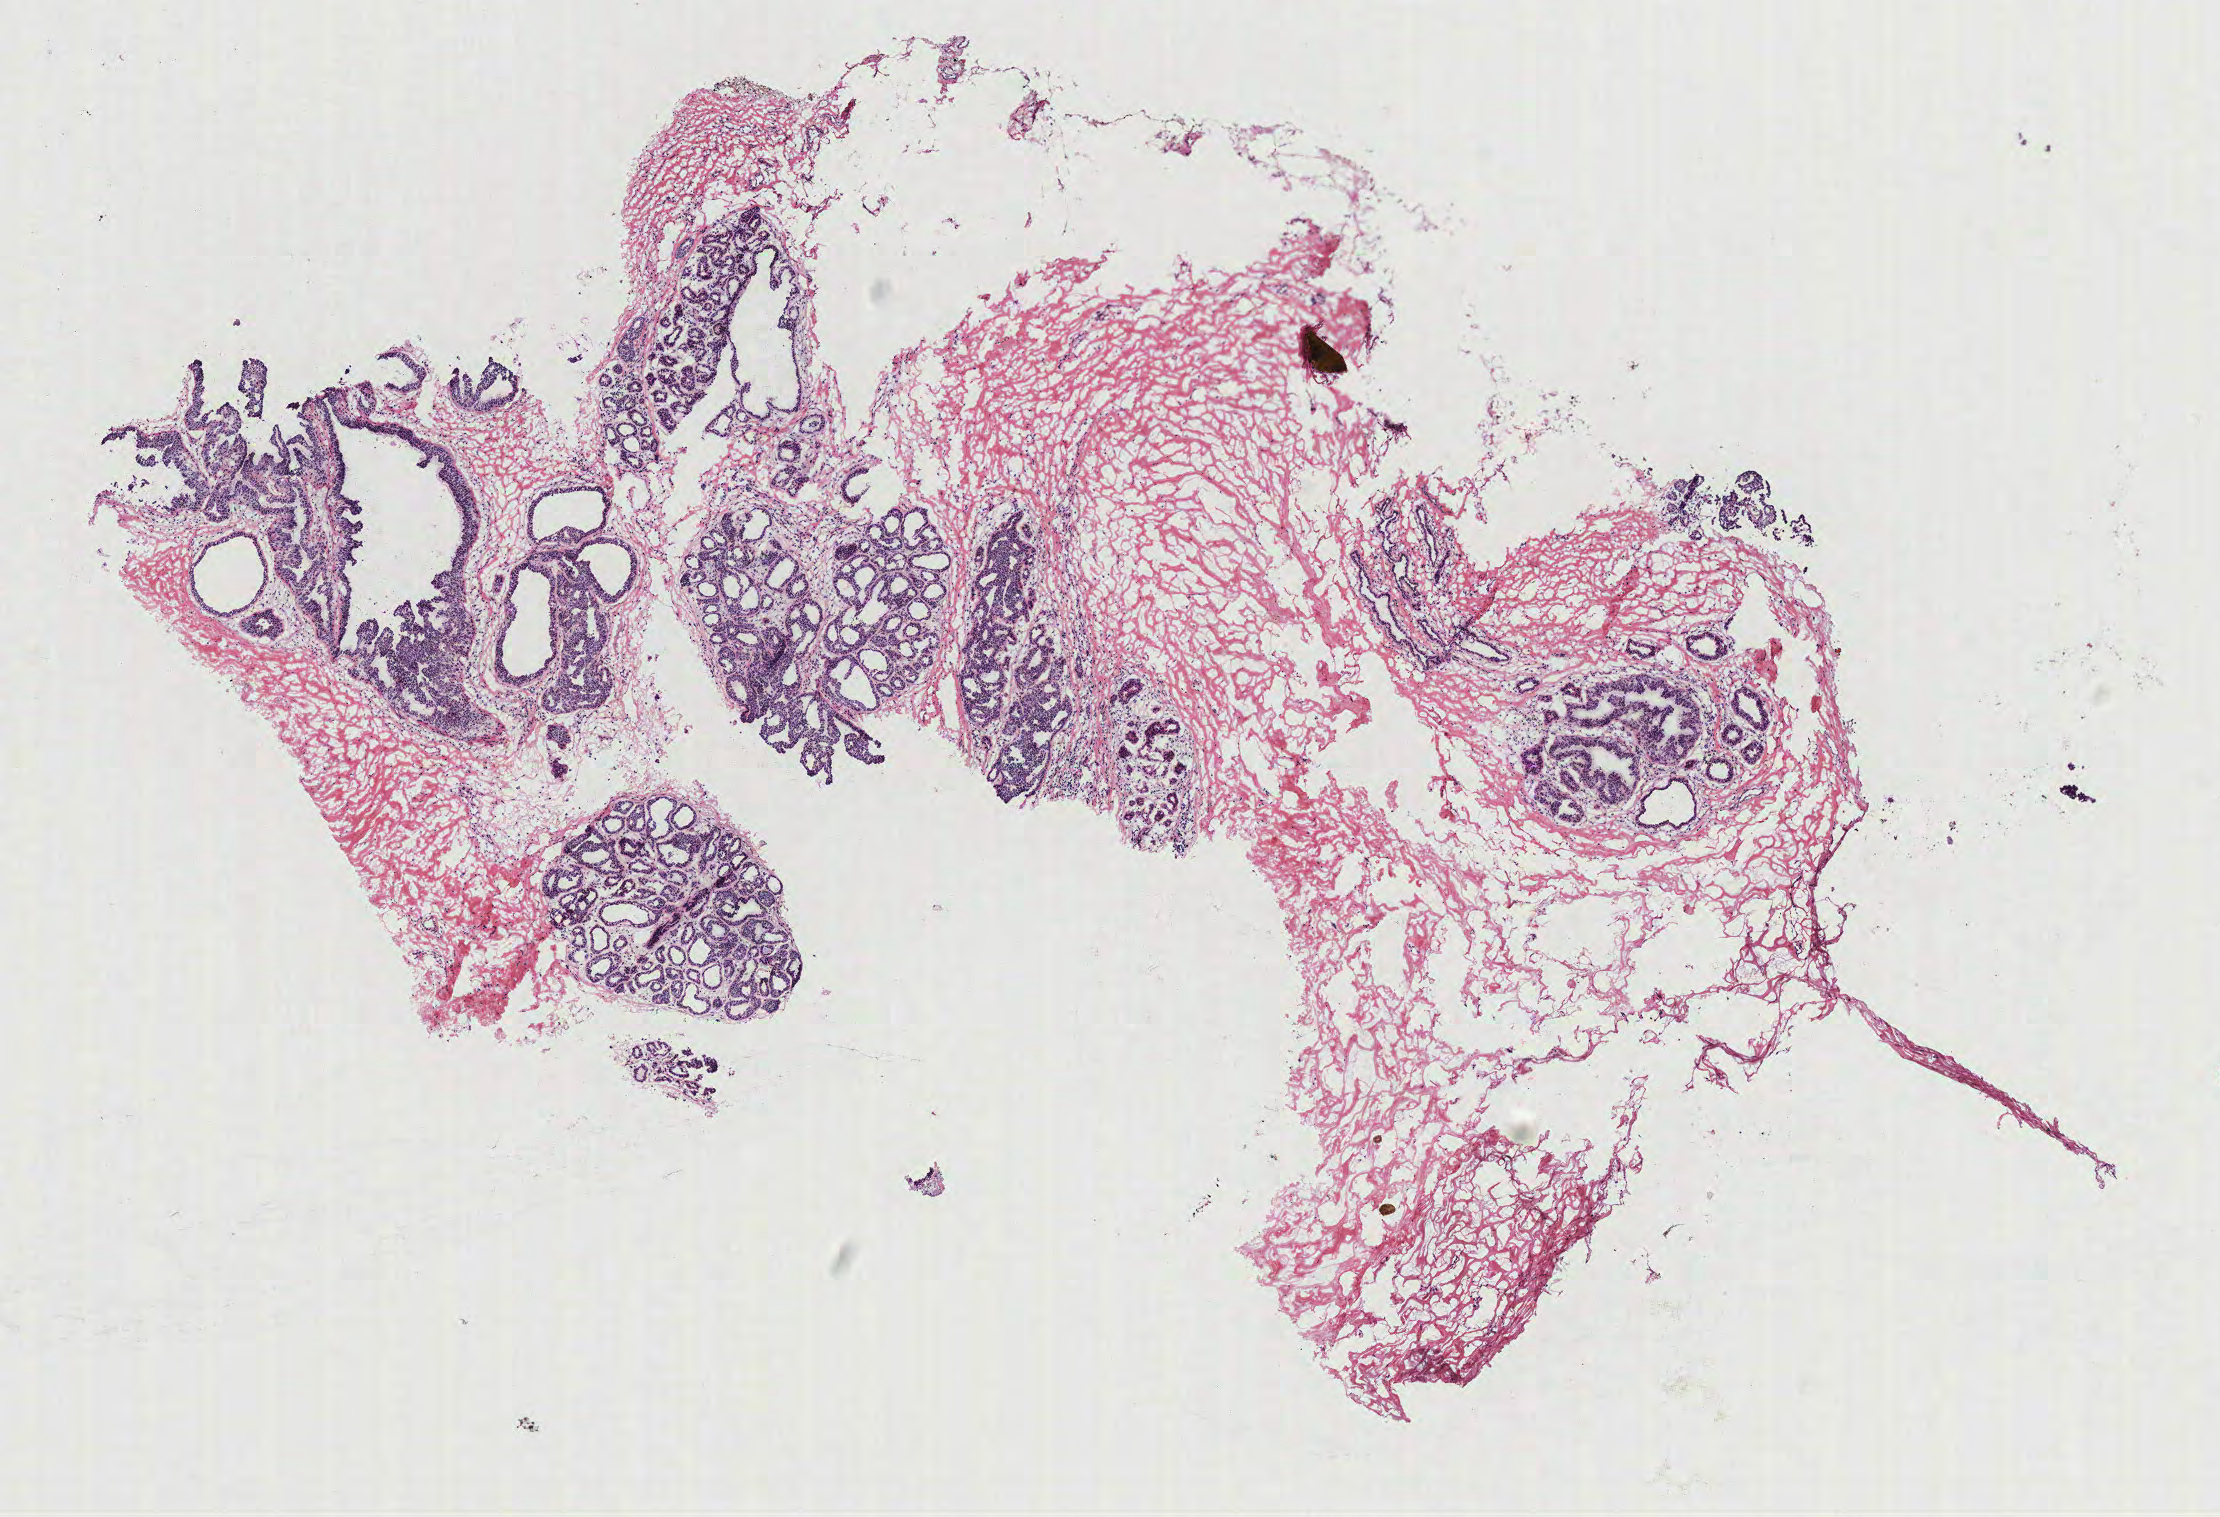
Digitized Hematoxylin and eosin (H&E) stained tissue section (whole slide), shown as a low-resolution overview of the whole scanned area (about 8.9 x 6.1 mm, acquisition: 40x scan); breast, tissue type not recorded. Patient: female, age 46 years.
Patient diagnosis: Infiltrating duct carcinoma, NOS.